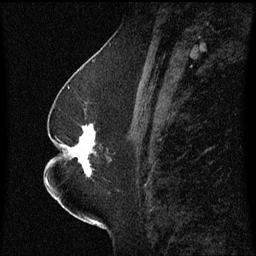
Breast MRI (dynamic contrast-enhanced), one sagittal slice. Position 29 of 60 along the scan axis. Dynamic contrast-enhanced series, image 2 of 3 at this slice position (ordered by acquisition). 1.5 T. TE 4.2 ms, TR 8.4 ms. 2.3 mm slice thickness. 256 × 256 image matrix, field of view 200 × 200 mm. Female patient, age 52 years. From the clinical record (not read from this slice): setting: breast cancer imaged before/during neoadjuvant chemotherapy; receptor status: HR-positive, HER2-negative.
Outlined on this slice (semi-automatic segmentation, software-assisted and operator-edited):
- analysis volume of interest (the breast-tissue region the enhancement analysis was run in; not a lesion): bounding box (x1, y1, x2, y2) in pixels: (65, 124, 113, 179)
- tumour enhancement mask (voxels above the 70 % enhancement threshold inside the analysis volume of interest): (67, 126, 97, 177)